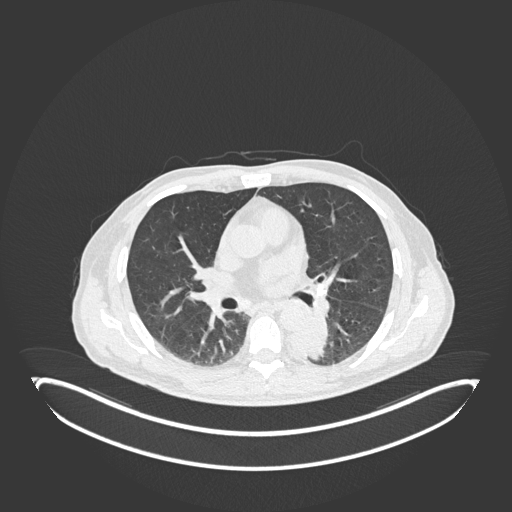
Chest CT, one axial slice. Slice 108 of 251 in the series (ordered by position). 120 kVp. Lung window (W 1500 / L -600 HU). 1 mm slice thickness. 512 × 512 image matrix, field of view 500 × 500 mm. Patient: male, 72 years. Case-level facts recorded for this patient, not image findings: clinical TNM (as recorded): T2b N0 M1.
Outlined on this slice (rectangle marked by the reading radiologist):
- lung tumour (recorded histology: adenocarcinoma): bounding box [x1, y1, x2, y2] px = [286, 316, 331, 361]